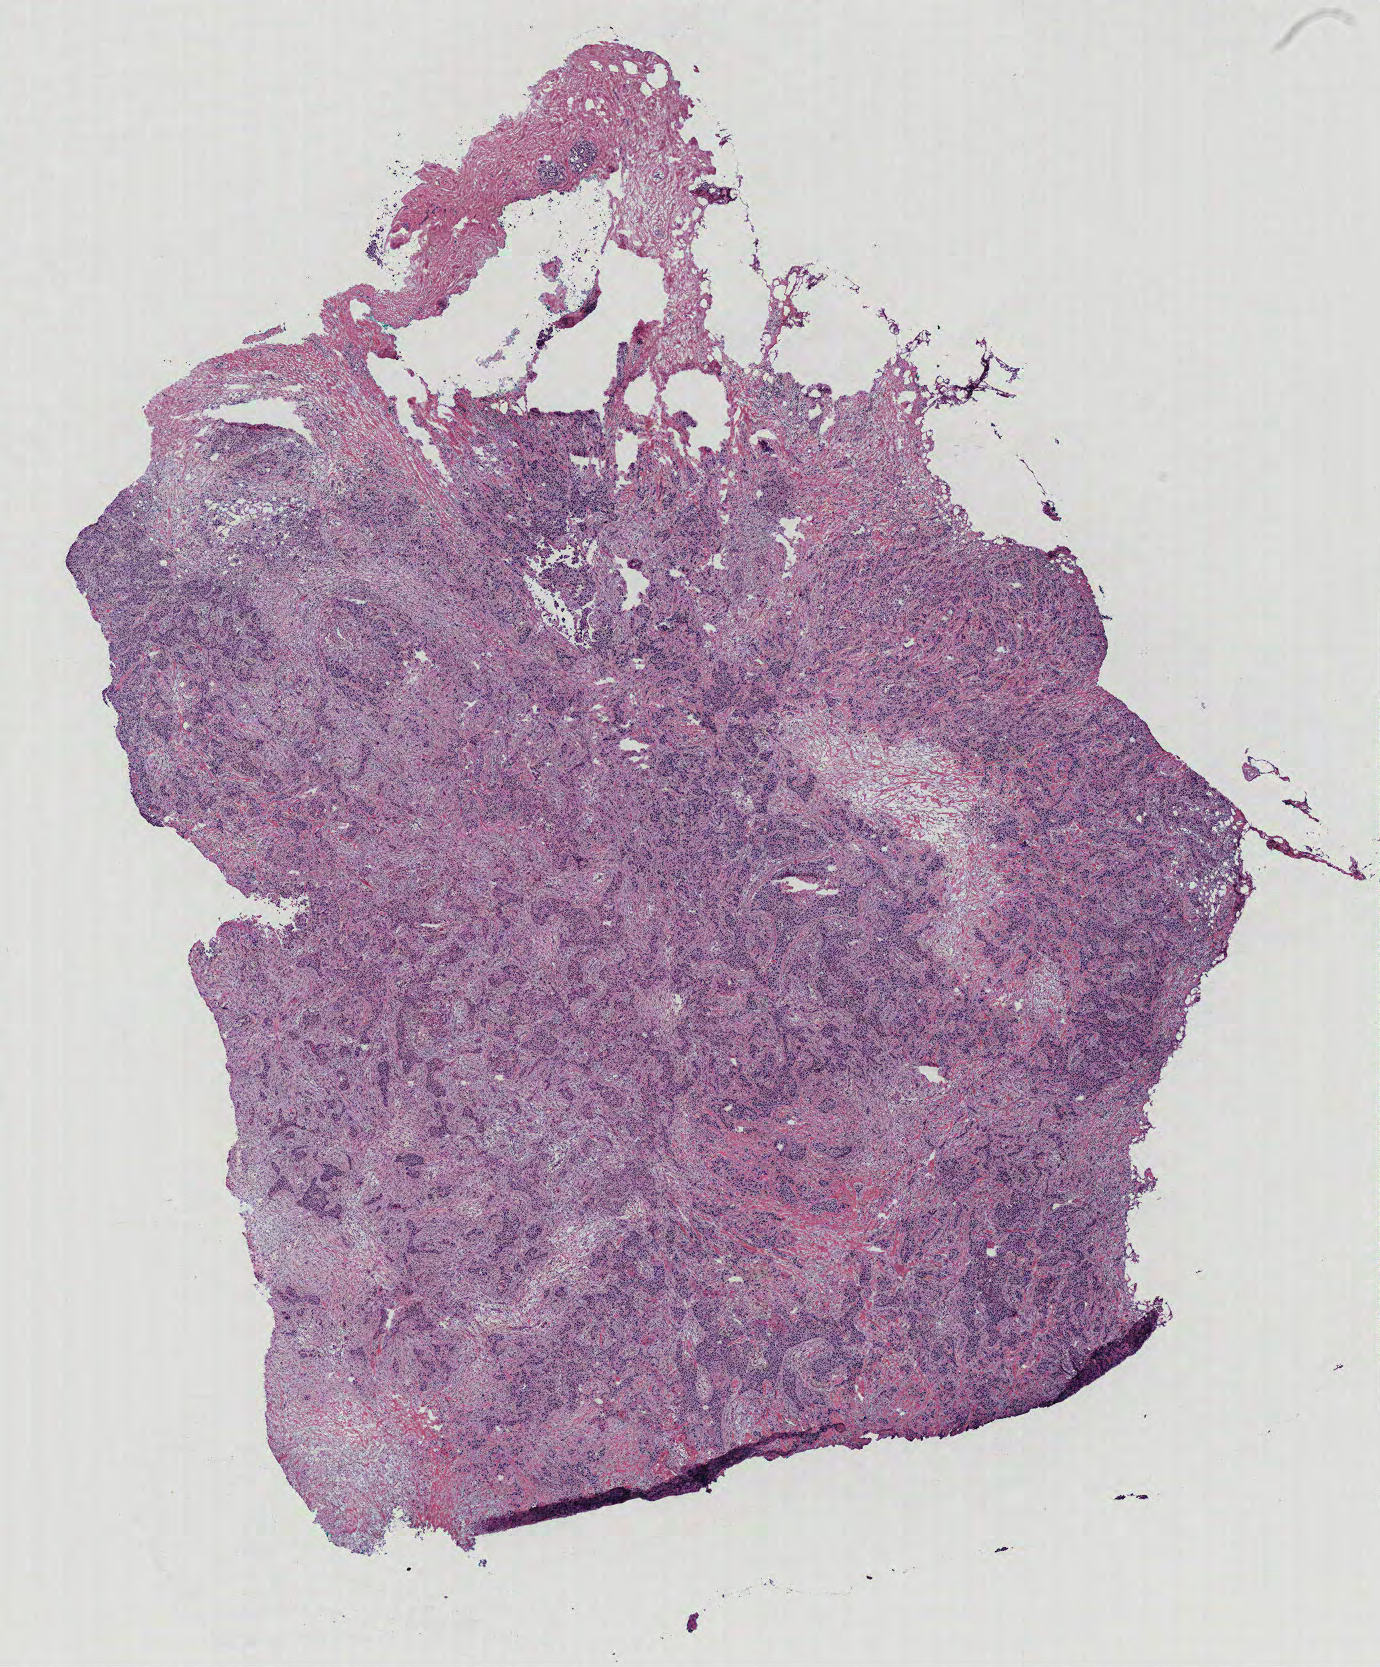
Whole-slide histology image, H&E — shown as a low-resolution overview of the whole scanned area (about 11.0 x 13.3 mm), breast, tissue type not recorded.
• patient diagnosis (cohort enrolment): breast cancer (breast)